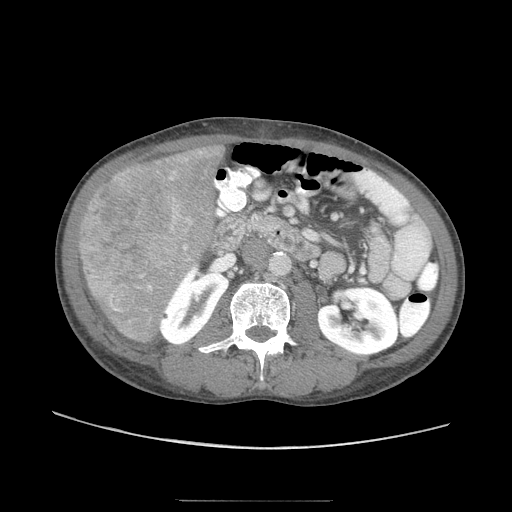
Contrast-enhanced abdominal CT (liver protocol), one axial slice. Slice 21 of 103 in the series (ordered by position). Reconstruction kernel STANDARD. 120 kVp. Soft-tissue window (W 400 / L 40 HU). 2.5 mm slice thickness. 512 × 512 image matrix. Case-level facts recorded for this patient, not image findings: diagnosis: hepatocellular carcinoma (patient treated with transarterial chemoembolisation; whether this scan precedes or follows treatment is not stated here); TNM stage (as recorded): Stage-IIIA; Child-Pugh class: A; tumour differentiation: moderately differentiated; tumour size: 16 cm.
Structures marked on this image (semi-automatically segmented with operator editing):
- liver parenchyma outside the tumour (the mass and vessels are separate outlines, so this box may not span the whole liver): bounding box (x1, y1, x2, y2) in pixels: (82, 142, 224, 344)
- mass: (77, 157, 195, 313)